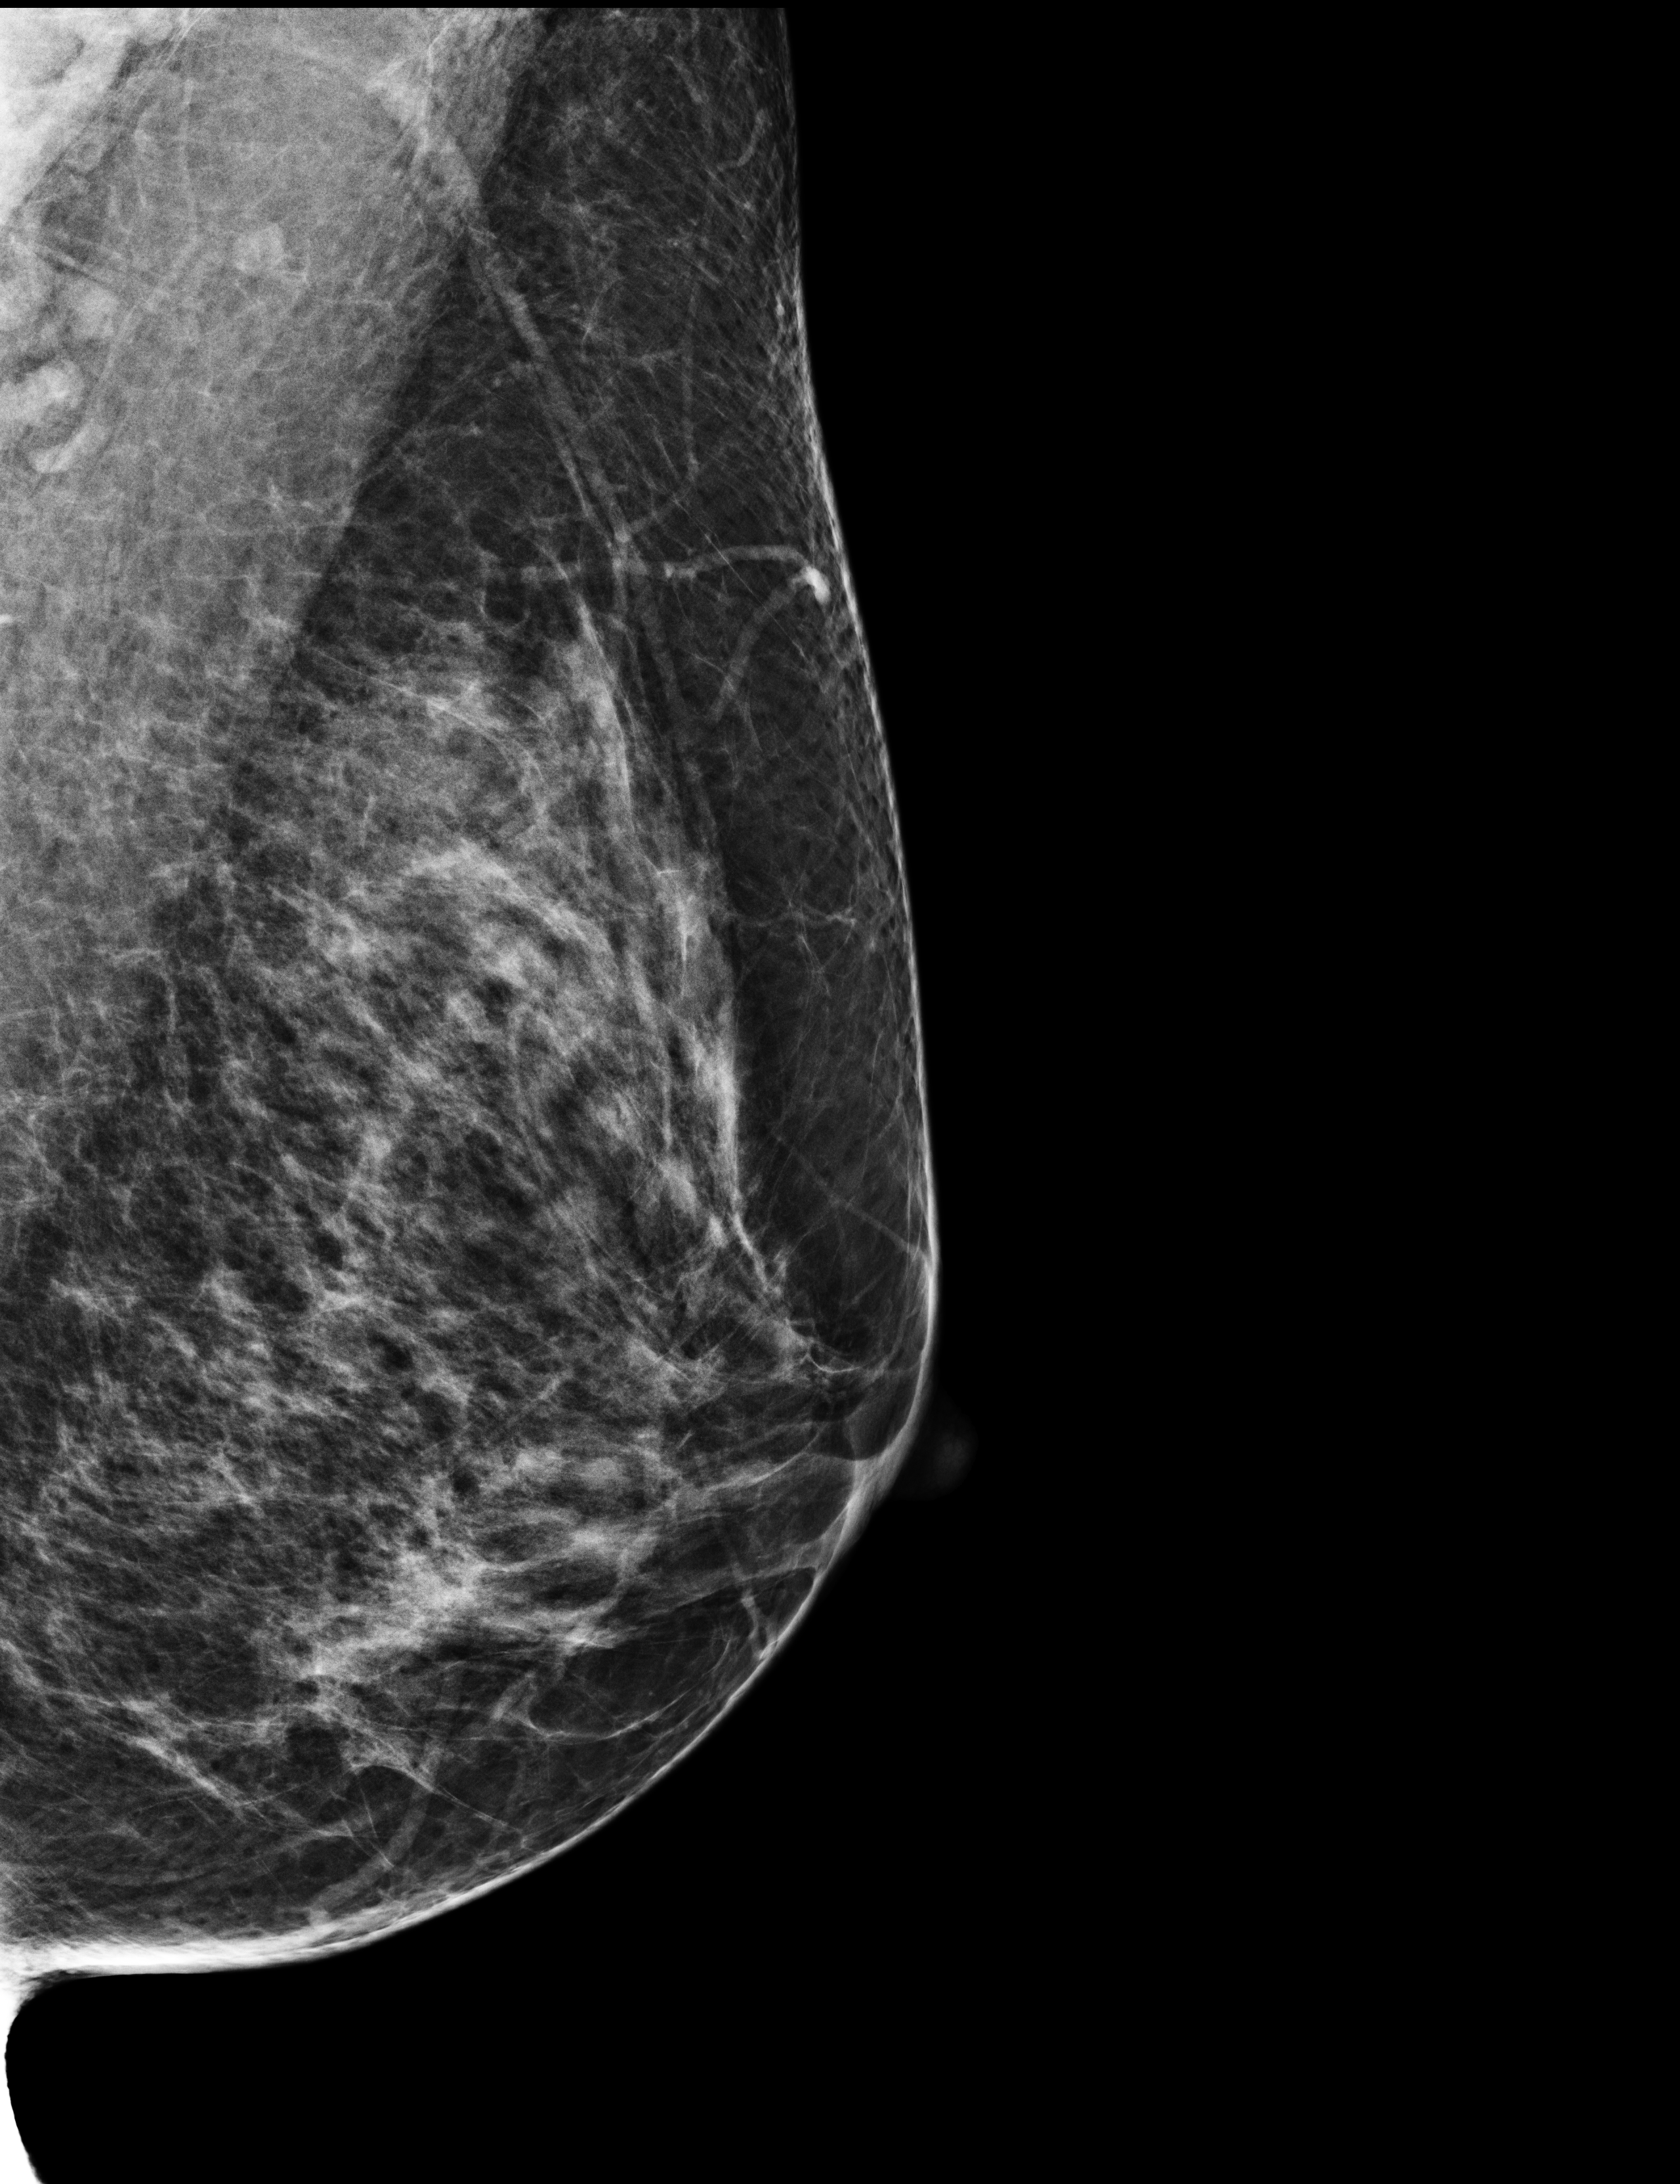
Annual screening mammography examination; compressed breast thickness 61 mm. Female patient, age 53 years.
Image type: full-field digital mammogram. Breast: left. Projection: mediolateral oblique (MLO) view.